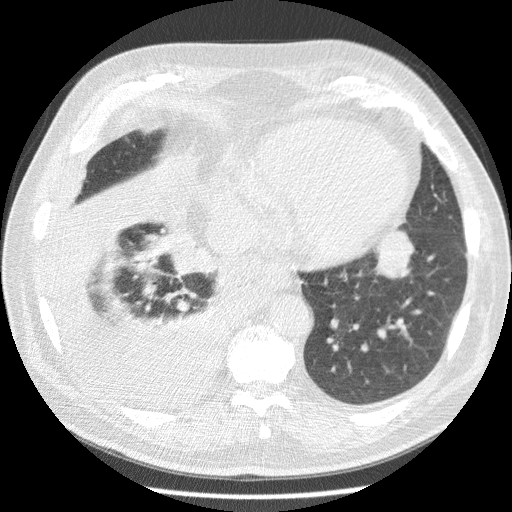
Low-dose screening chest CT, one axial slice; slice 61 of 180 in the series (ordered by position); reconstruction kernel STANDARD; 120 kVp; lung window (W 1500 / L -600 HU); 2.5 mm slice thickness; 512 × 512 image matrix, field of view 355 × 355 mm.
Outlined on this slice (outlined manually by an expert reader):
- lesion 1 (tumor, lower lobe of left lung): bounding box [x1, y1, x2, y2] px = [376, 231, 414, 278]